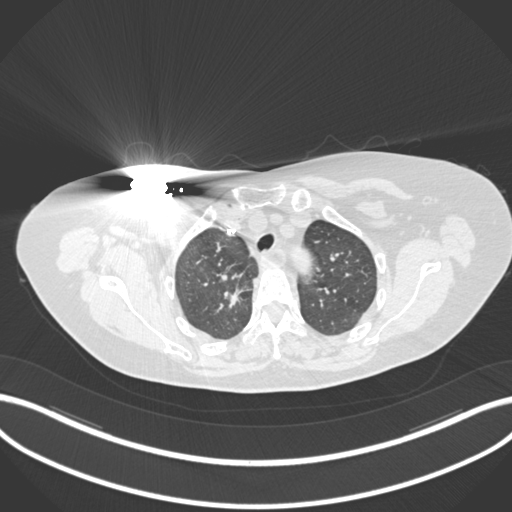
Chest CT, one axial slice; position 145 of 176 along the scan axis; reconstruction kernel B30f; 120 kVp; lung window (W 1500 / L -600 HU); 1 mm slice thickness; 512 × 512 image matrix, field of view 400 × 400 mm. Female patient, age 72 years. Case-level facts recorded for this patient, not image findings: clinical TNM (as recorded): T1c N0 M0.
Outlined on this slice (bounding box drawn by a radiologist):
- lung tumour (recorded histology: adenocarcinoma): bounding box [x1, y1, x2, y2] px = [212, 280, 255, 314]